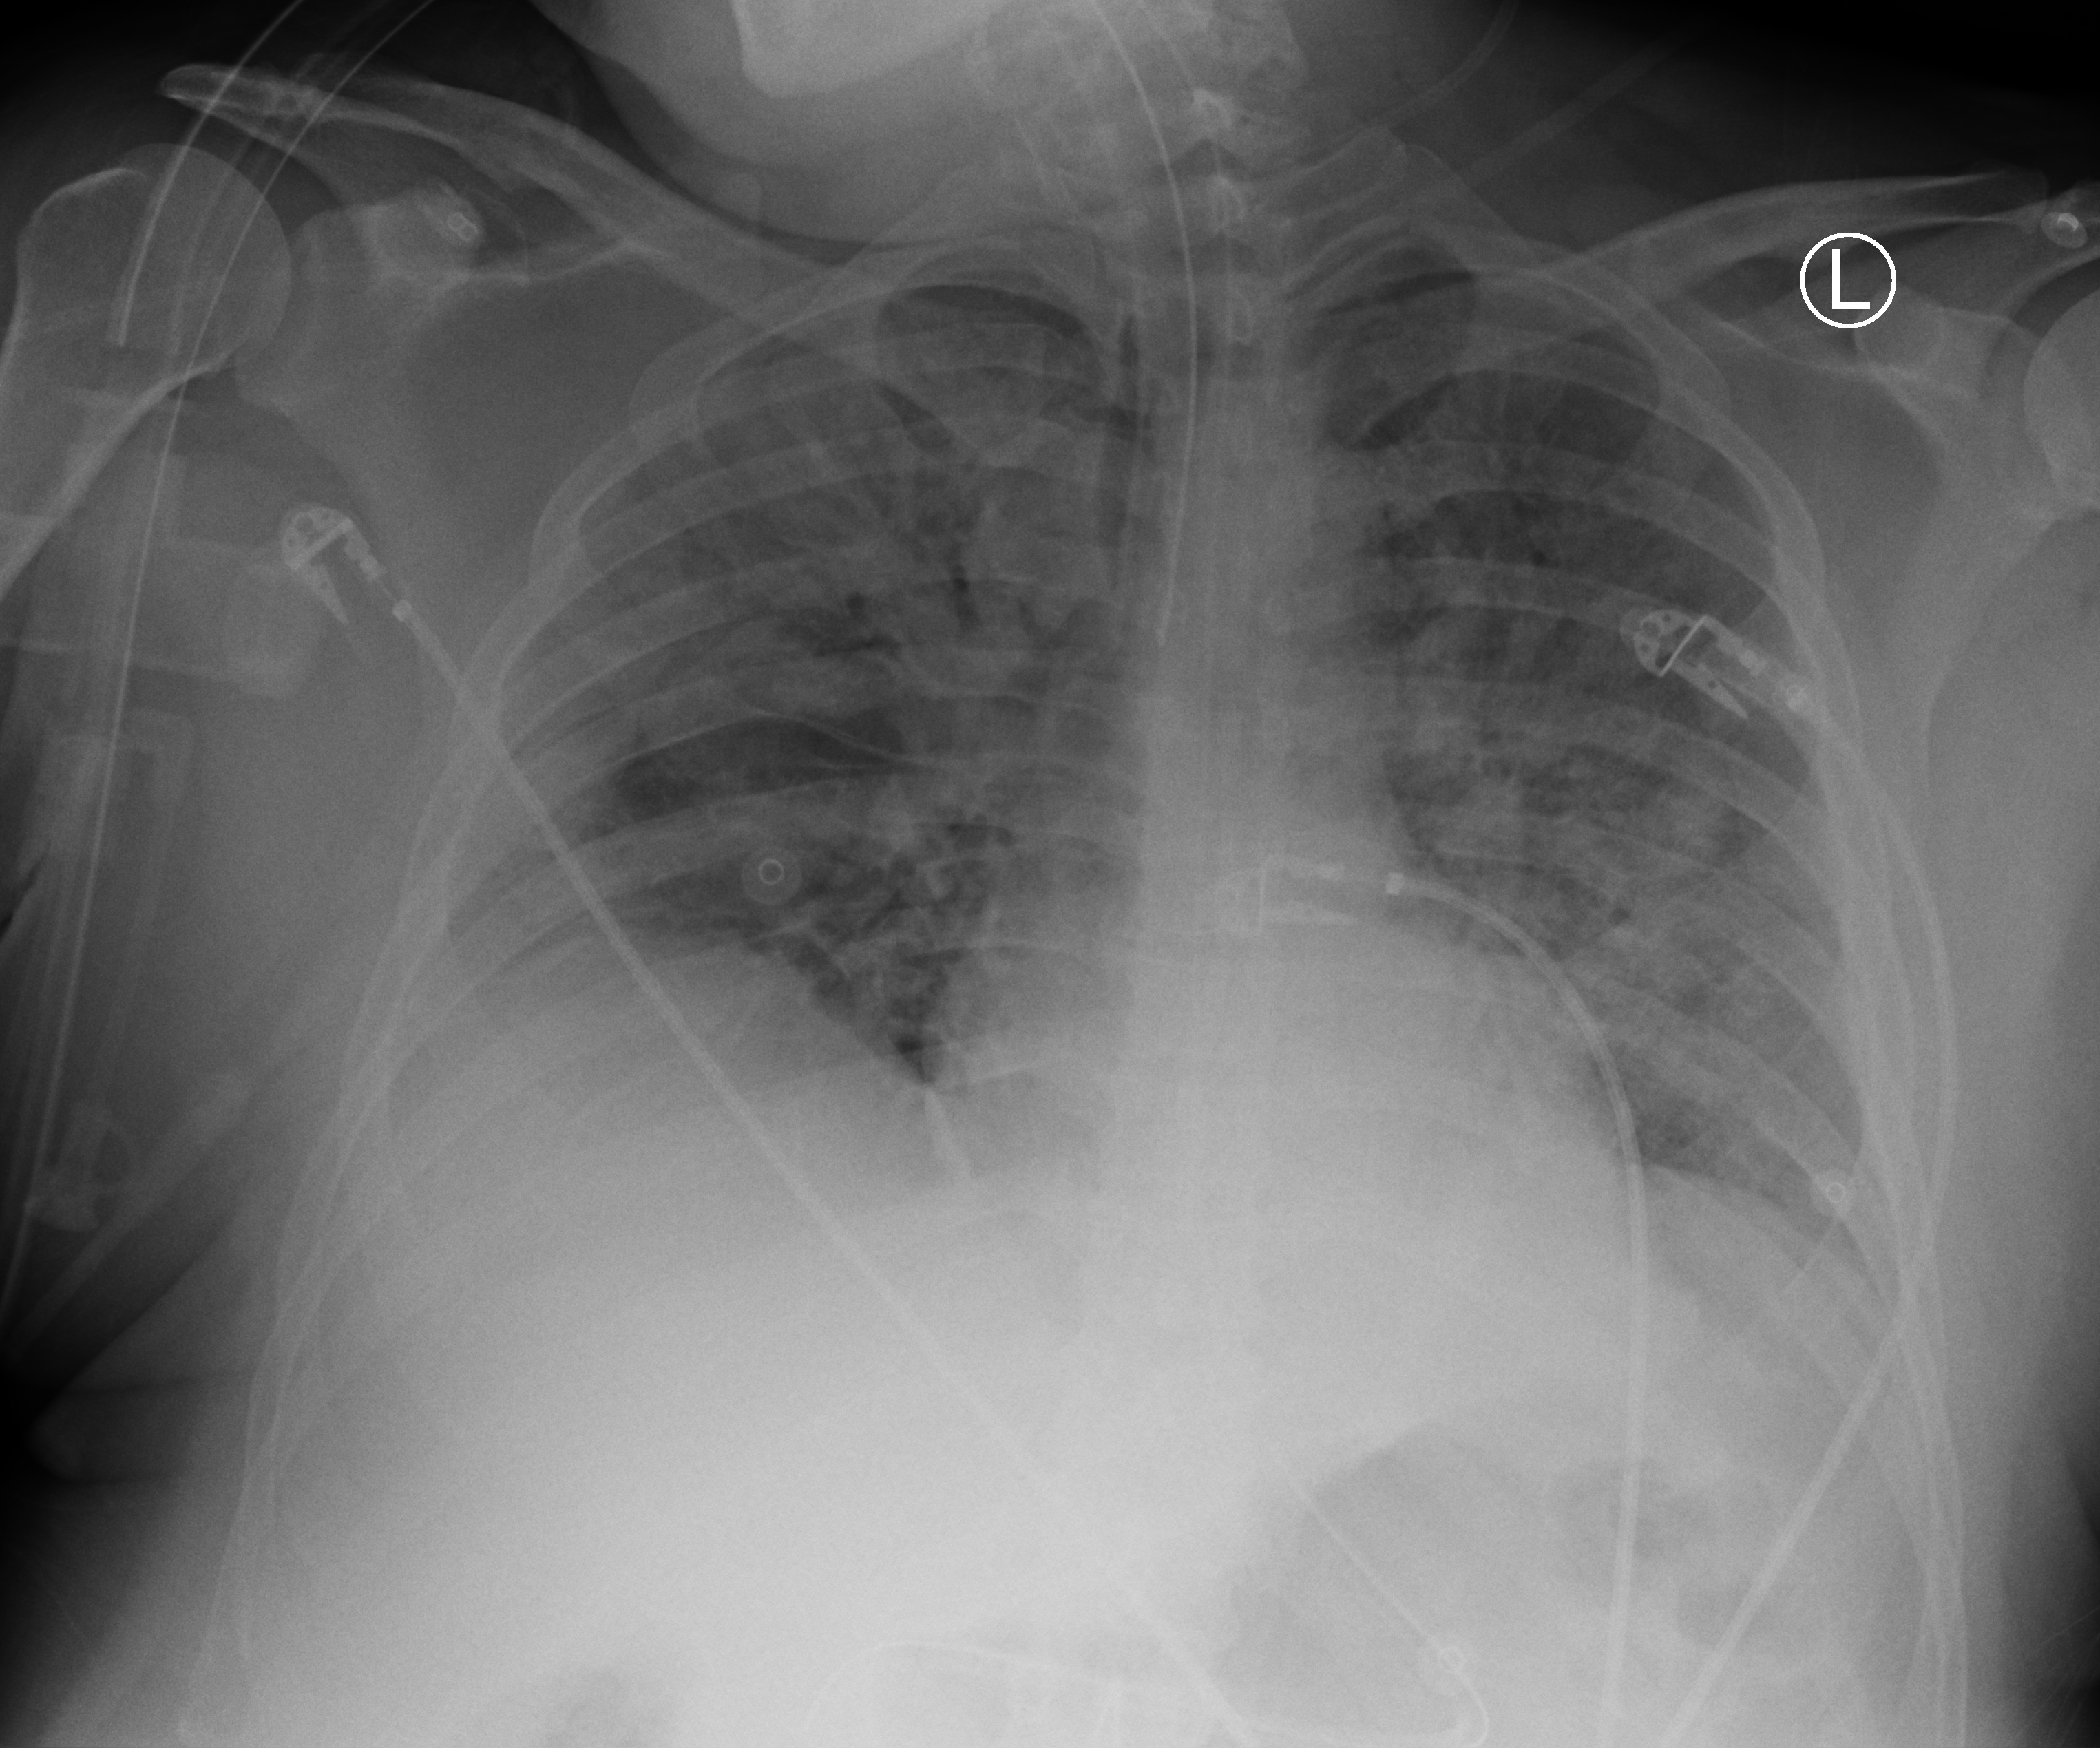
Chest X-ray (portable). Male patient hospitalised with COVID-19, age 18–59 years.
From the hospital-stay record, not from the radiograph (when in the stay this image was taken is not recorded): admitted to intensive care during this hospital stay: yes; mechanically ventilated during this hospital stay: yes; chronic kidney disease (admission record): no.